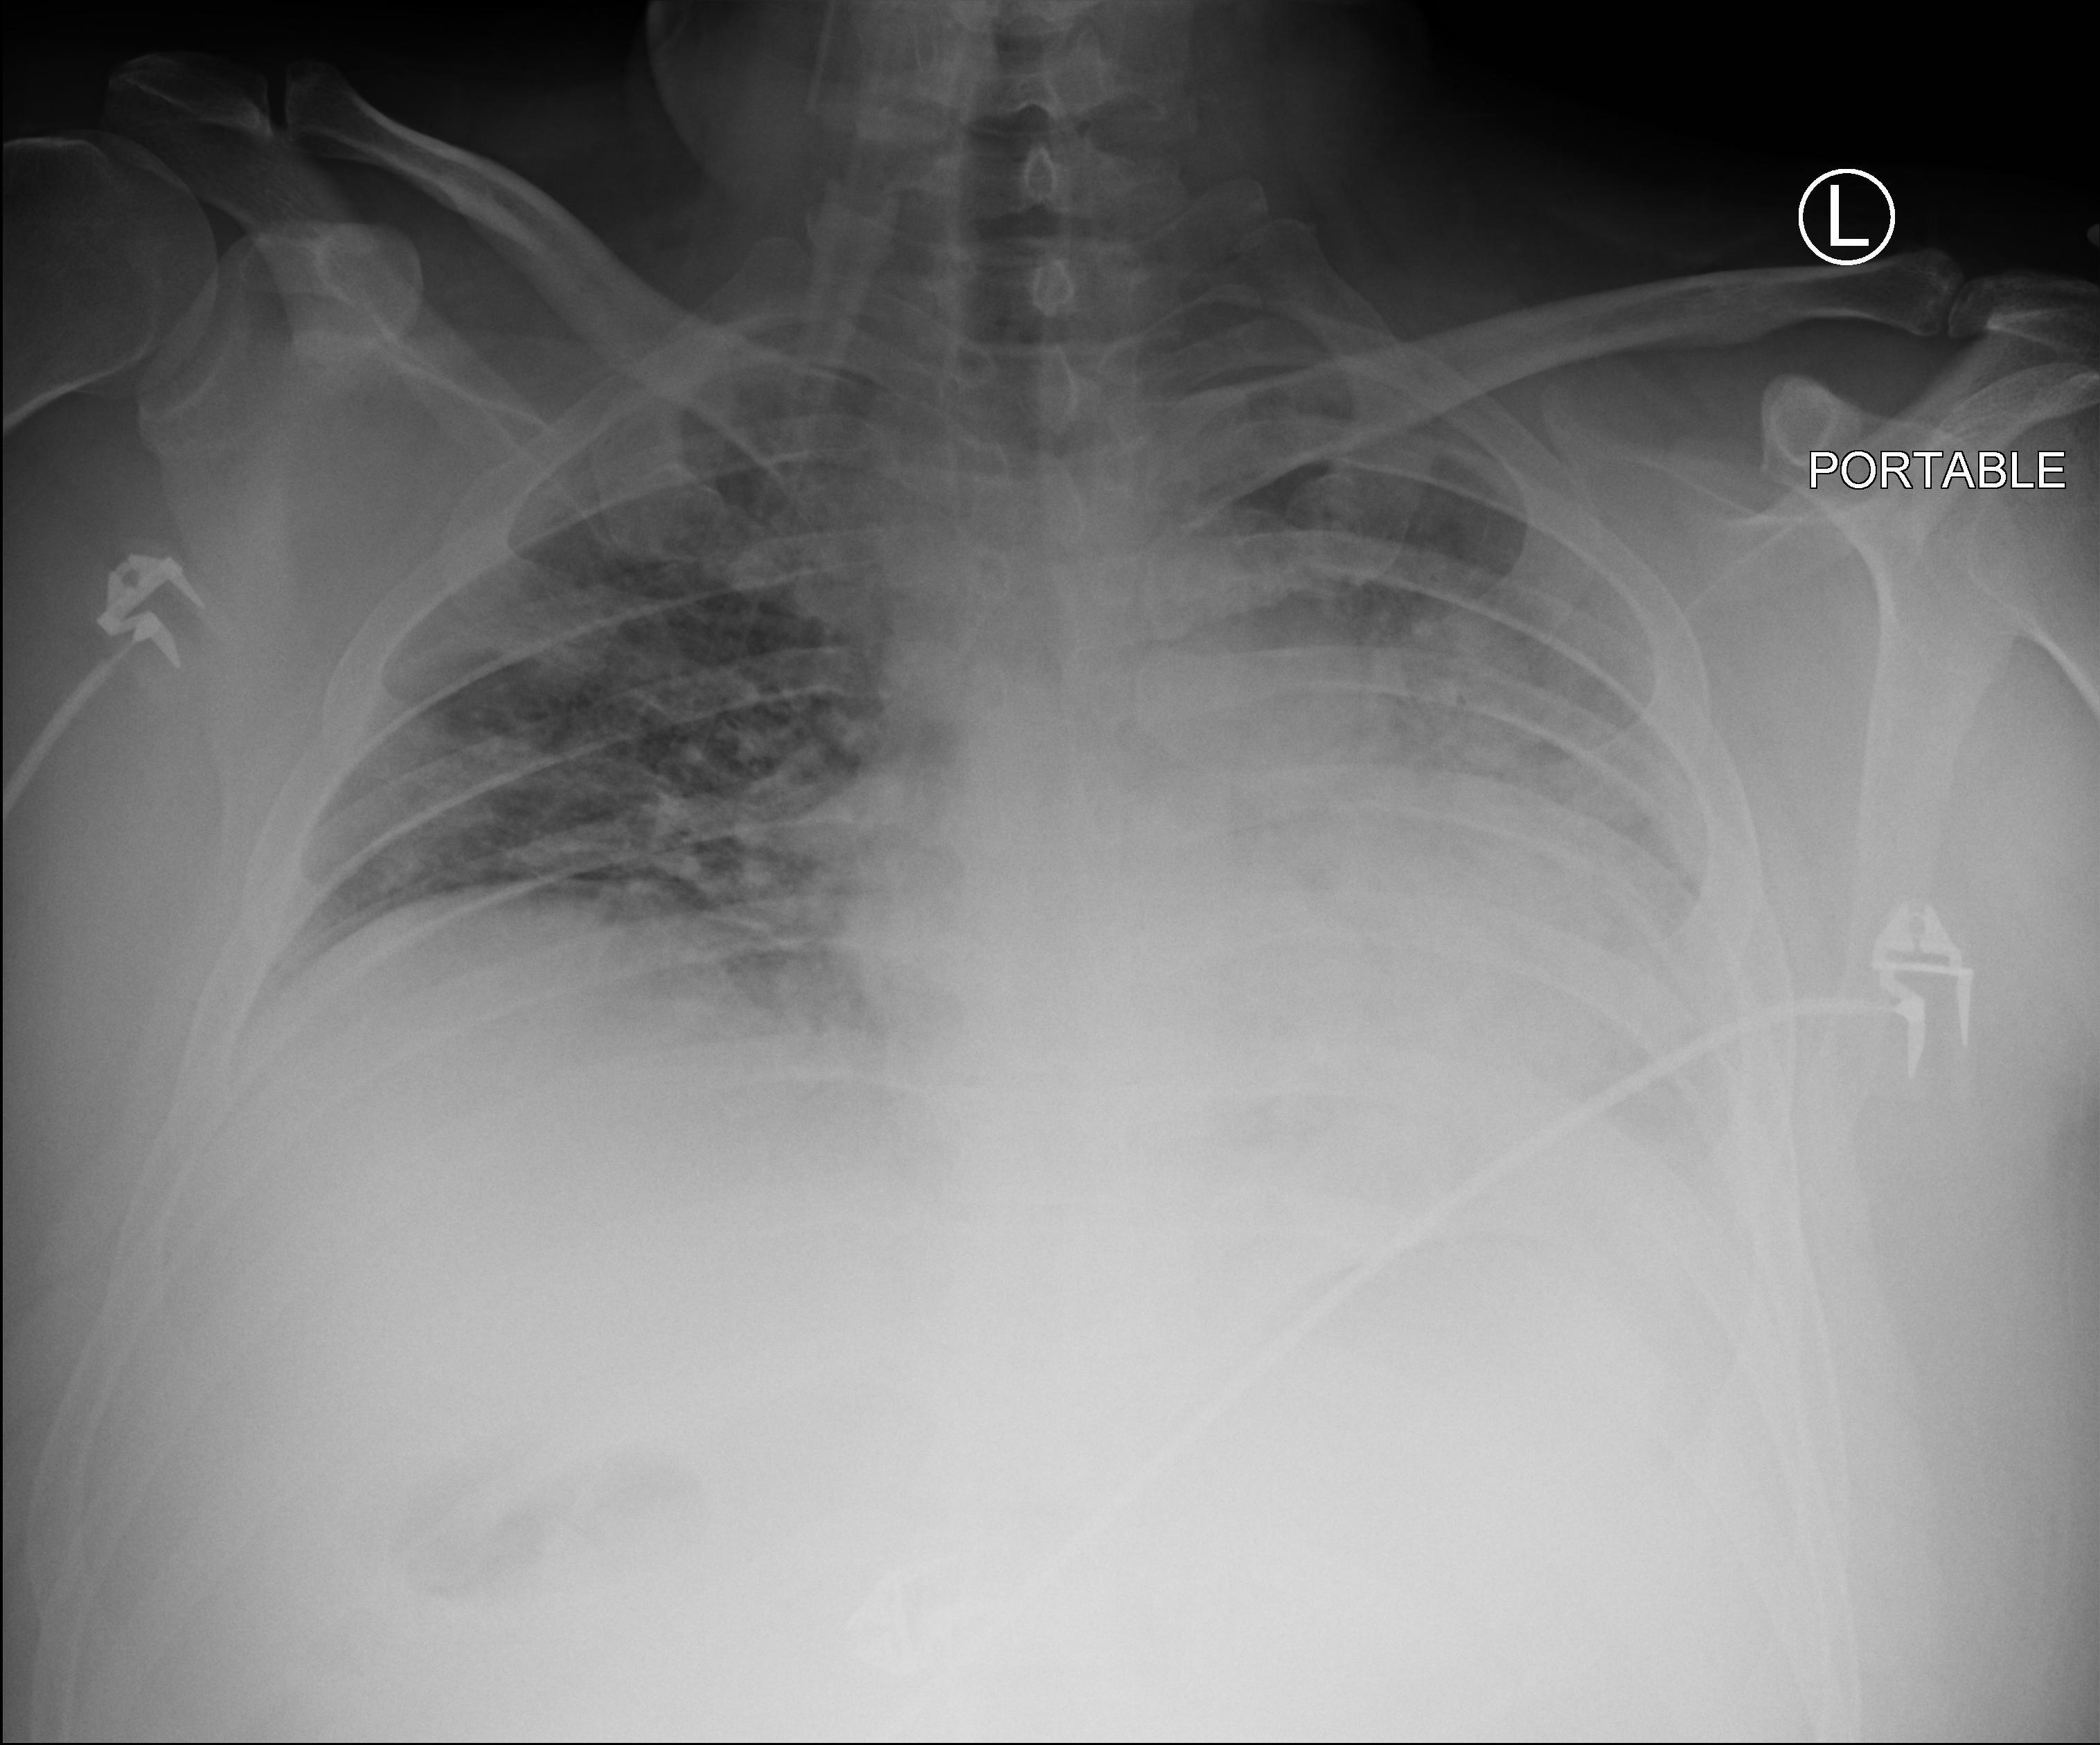
Portable chest radiograph; anteroposterior (AP) projection. Male patient hospitalised with COVID-19, age 18–59 years.
Hospital-stay facts (about this admission, not read from this image; timing relative to this image not recorded): smoking status (admission record): never; other chronic lung disease (admission record): no; admitted to intensive care during this hospital stay: no.